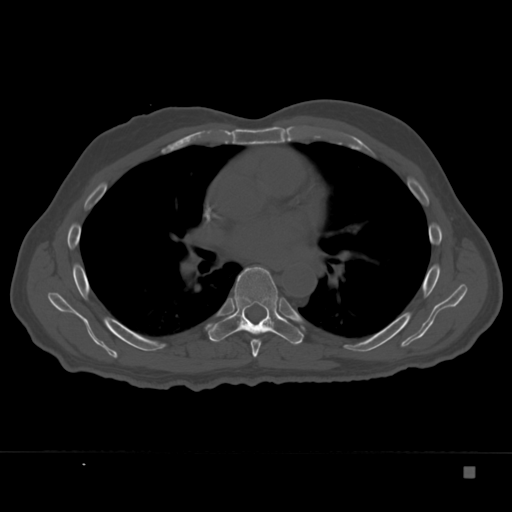
CT including the spine, one axial slice; slice 228 of 332 in the series (ordered by position); reconstruction kernel Br40s; 120 kVp; bone window (W 1800 / L 400 HU); 1.5 mm slice thickness; 512 × 512 image matrix. Male patient, age 72 years. Case-level facts recorded for this patient, not image findings: primary cancer: skeletal.
Outlined on this slice (semi-automatic segmentation, software-assisted and operator-edited):
- T6 vertebra: bounding box <251,339,261,358> (left, top, right, bottom; pixels)
- T7 vertebra: <207,267,304,345>